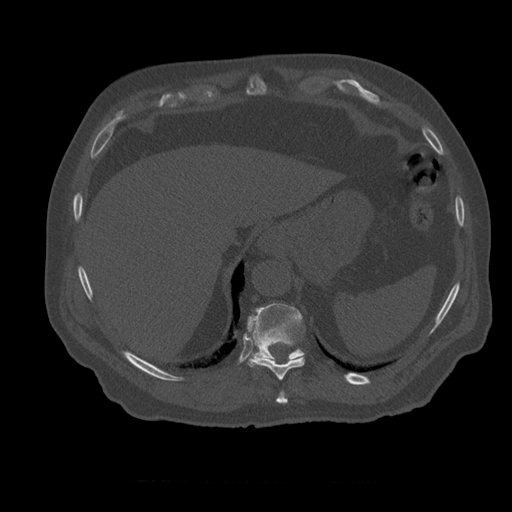
CT including the spine, one axial slice. Reconstruction kernel STANDARD. Bone window (W 1800 / L 400 HU). 1.25 mm slice thickness. 512 × 512 image matrix, field of view 407 × 407 mm. Patient age 73 years. From the clinical record (not read from this slice): primary cancer: prostate; vertebrae with lytic lesions (as recorded): L2.
Outlined on this slice (semi-automatically segmented with operator editing):
- T10 vertebra: bounding box (x1, y1, x2, y2) in pixels: (248, 337, 305, 381)
- T11 vertebra: (248, 304, 305, 361)
- T9 vertebra: (276, 392, 289, 404)